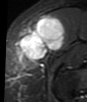
MRI of an extremity soft-tissue mass, one axial slice. Position 20 of 48 along the scan axis. STIR. MR volume resampled by the dataset authors to the PET/CT grid (not the native acquisition matrix). 87 × 102 image matrix, field of view 85 × 100 mm. Female patient. Case-level facts recorded for this patient, not image findings: histological type: synovial sarcoma; grade: intermediate; site of the primary tumour: right thigh.
Outlined on this slice (expert contour drawn on MRI and transferred to this co-registered scan by the dataset authors):
- gross tumour volume including surrounding oedema: bounding box [x1, y1, x2, y2] px = [15, 15, 66, 64]
- gross tumour volume (mass): [15, 15, 66, 64]